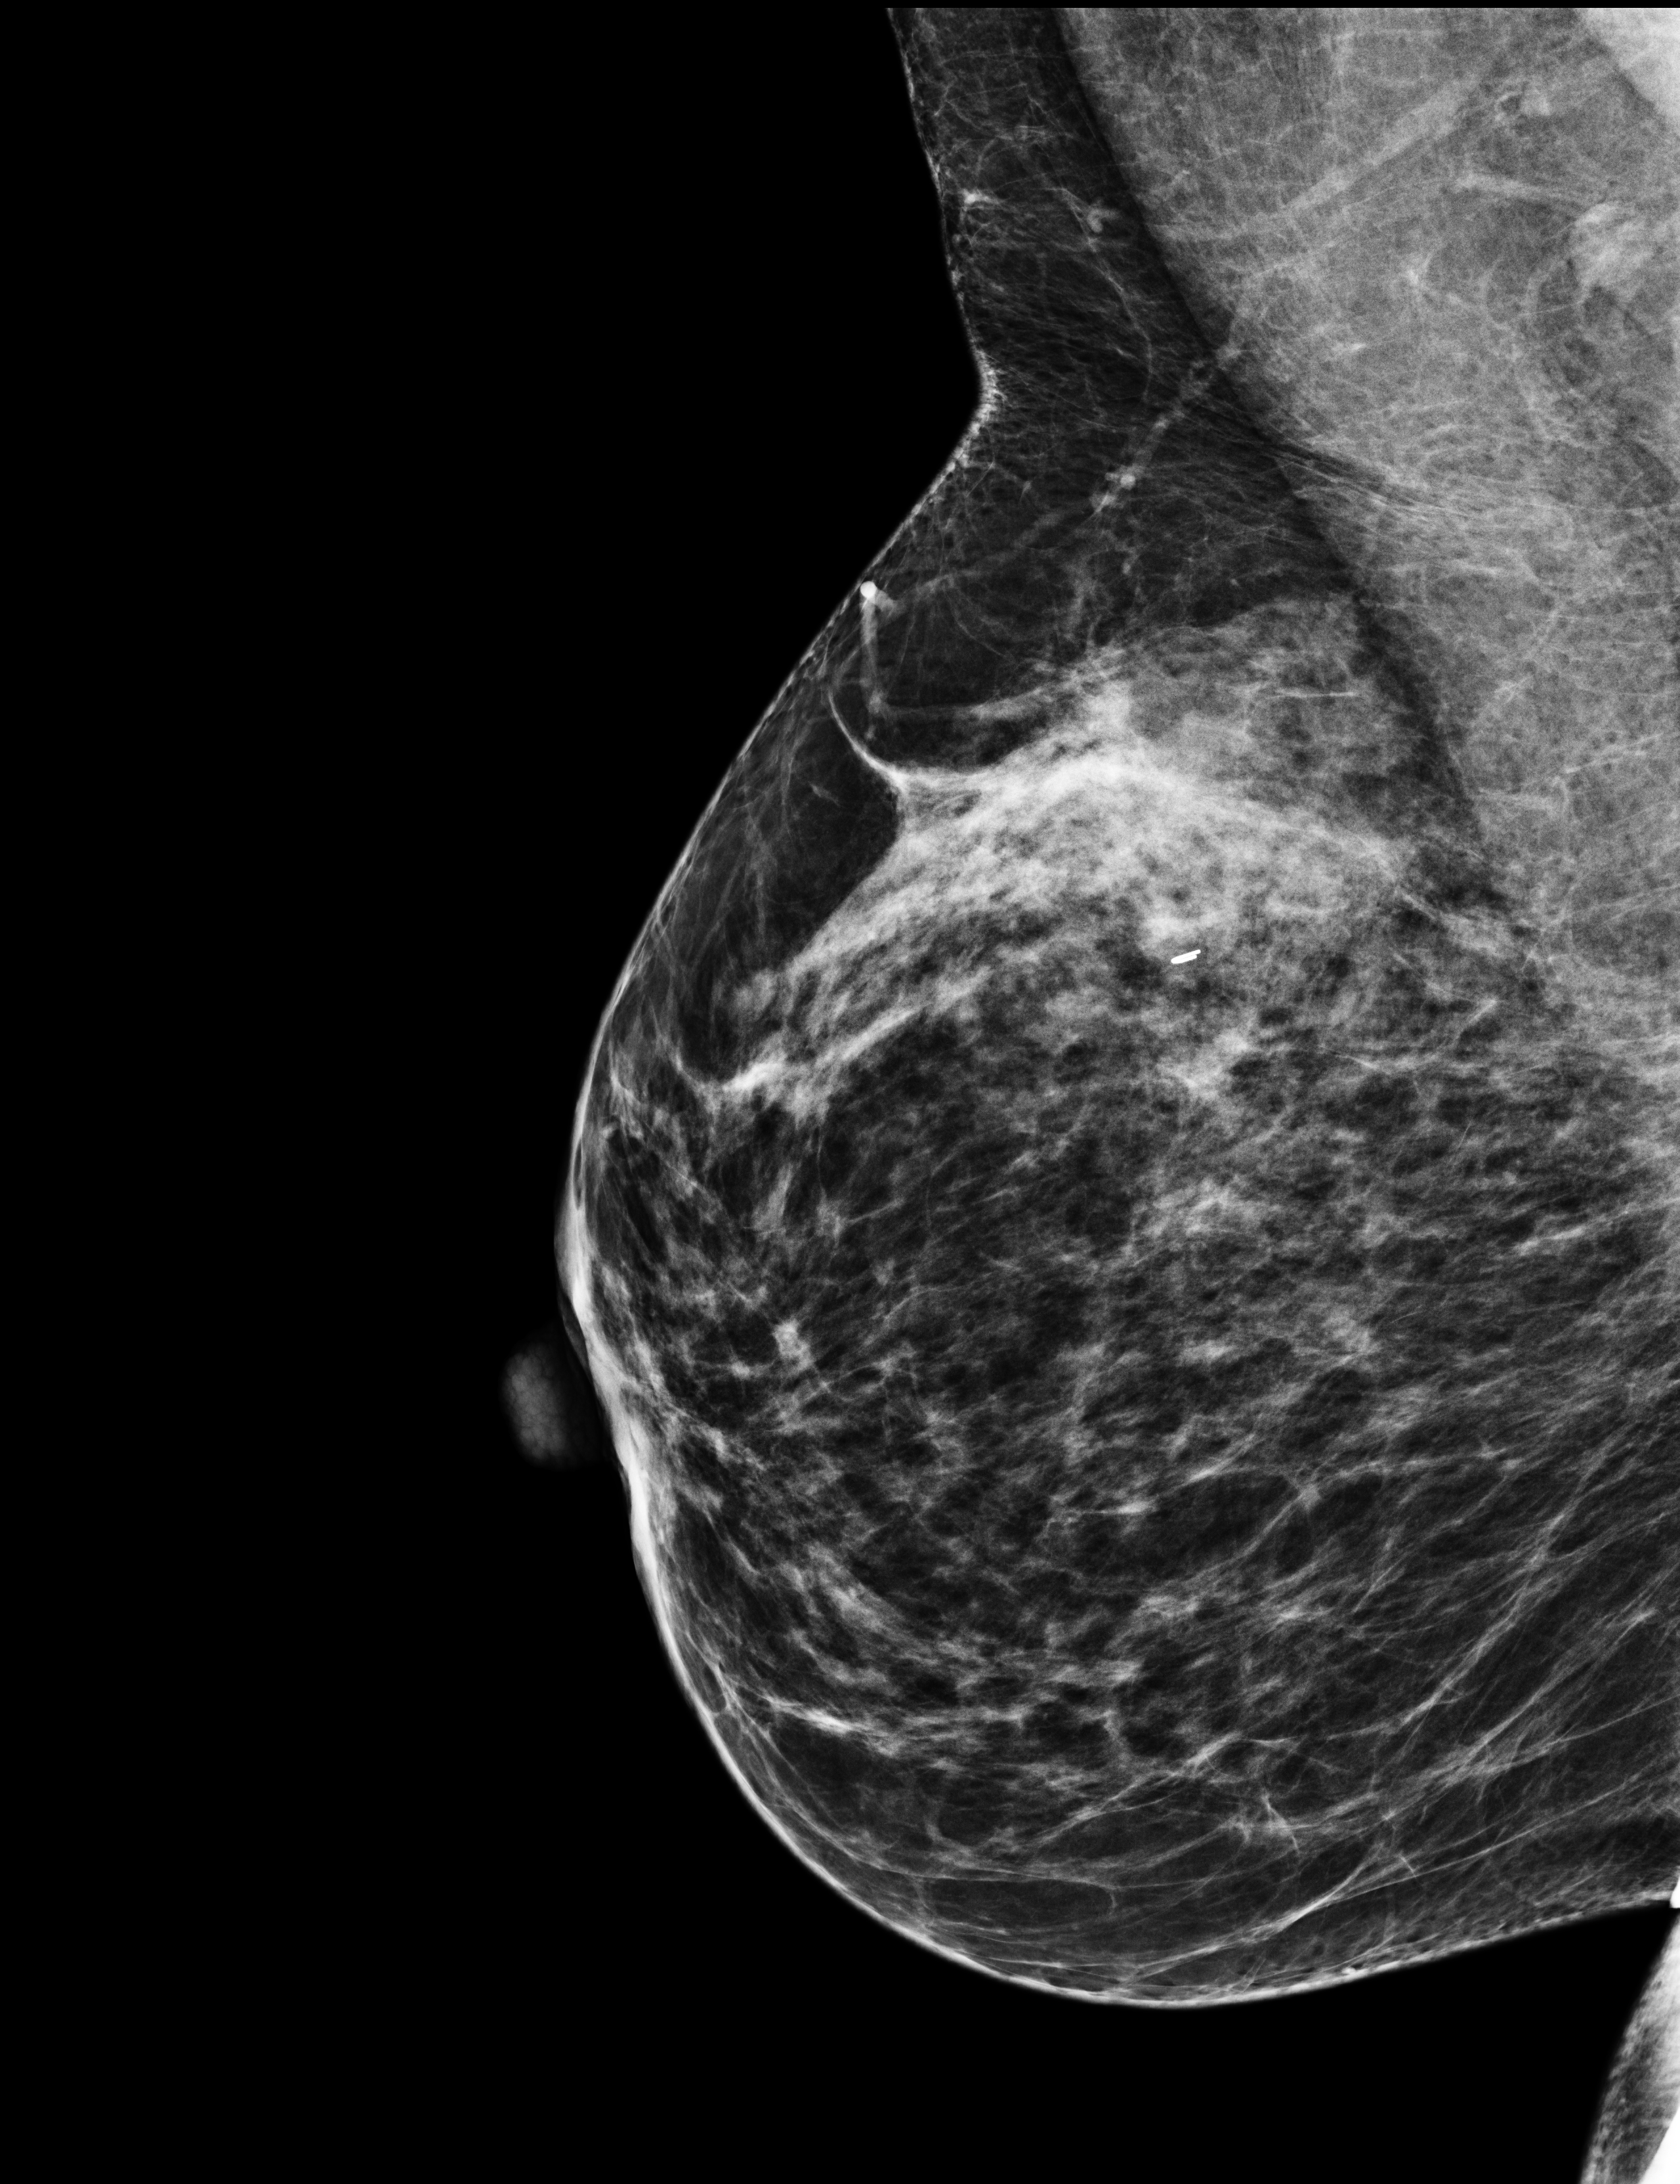
Digital mammogram (FFDM), right breast, mediolateral oblique (MLO) view, screening examination, system: Selenia Dimensions. Patient: female, 62 years.
- breast density at the screening exam (both breasts): heterogeneously dense (BI-RADS density category c)
- final BI-RADS category for the screening round (tomosynthesis exam, both breasts): category 1
- recall: no recall after this screen